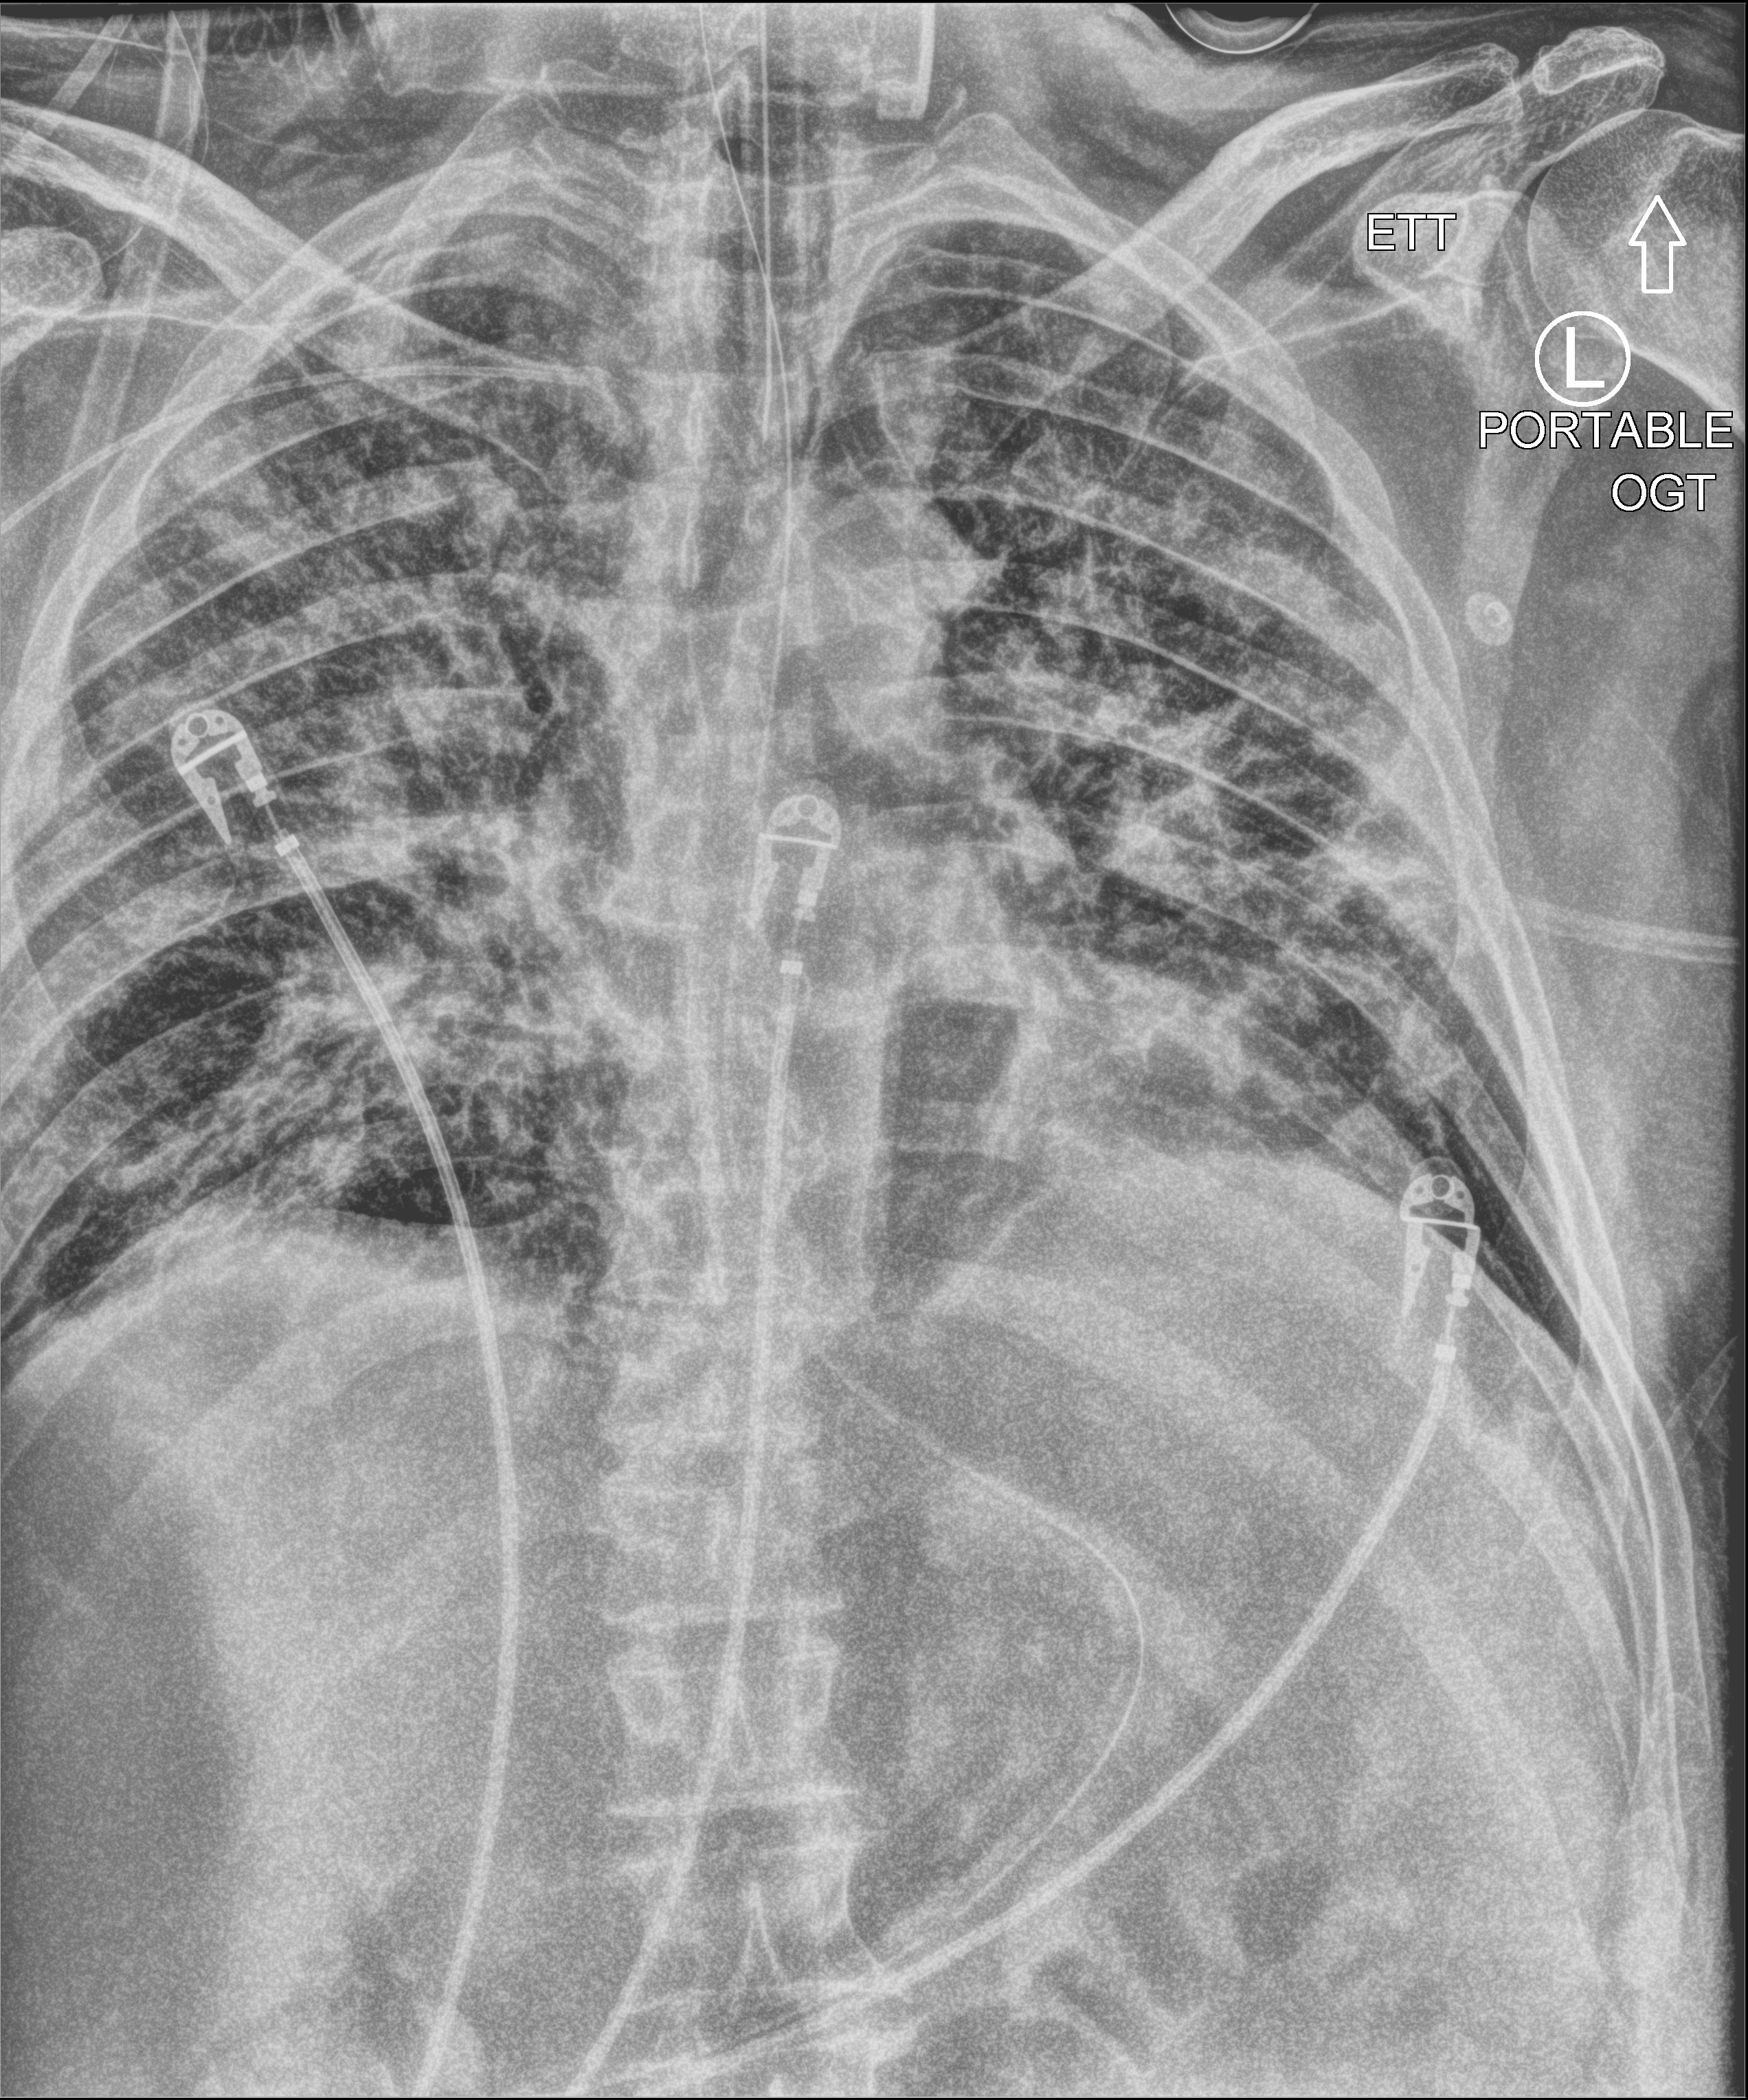
Portable chest radiograph; anteroposterior (AP) projection. Patient hospitalised with COVID-19; male, aged 60–74 years.
Admission-level facts for this patient (not findings on this image; timing relative to this image not recorded): diabetes (admission record): yes.